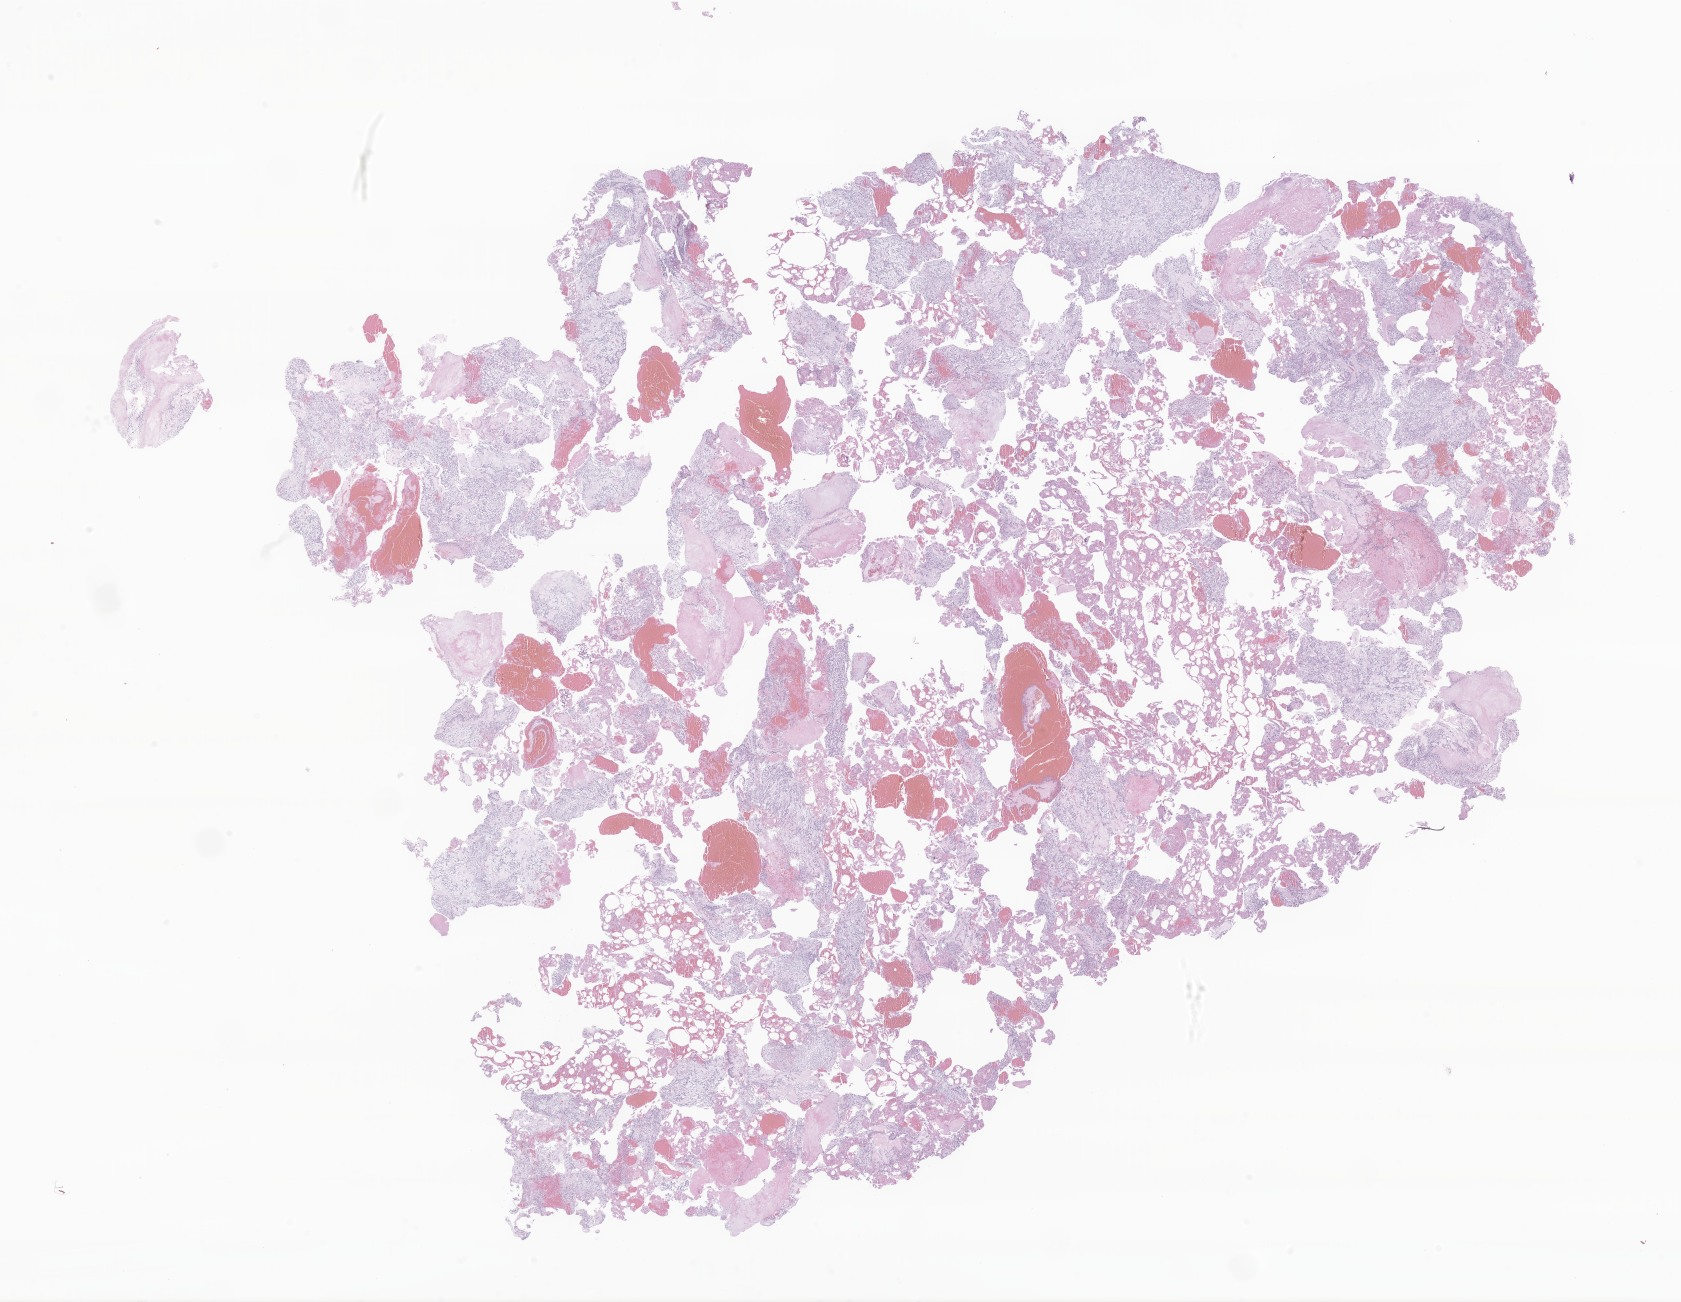
H&E whole-slide image of tumor tissue from the vertebral column — low-resolution overview of the scanned area, about 28.3 x 22.0 mm. FFPE section. Male patient, age 160 months (13 years 4 months).
Recorded diagnosis: Myxopapillary ependymoma.